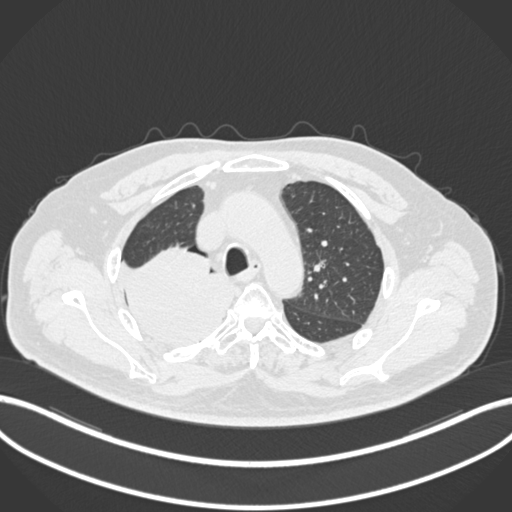
Chest CT, one axial slice. Position 155 of 218 along the scan axis. Lung window (W 1500 / L -600 HU). 512 × 512 image matrix. Patient: male, 68 years. From the clinical record (not read from this slice): clinical TNM (as recorded): T2a N0 M0.
Structures marked on this image (rectangle marked by the reading radiologist):
- lung tumour (recorded histology: adenocarcinoma): bounding box (x1, y1, x2, y2) in pixels: (122, 247, 237, 347)